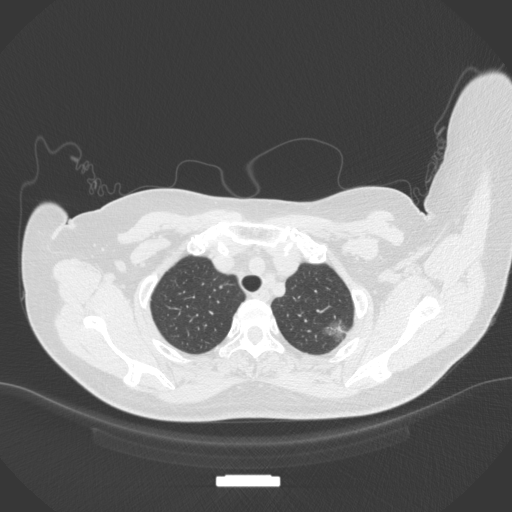
Chest CT, one axial slice; slice 315 of 386 in the series (ordered by position); 120 kVp; lung window (W 1500 / L -600 HU); 1 mm slice thickness; 512 × 512 image matrix, field of view 400 × 400 mm. Female patient, age 58 years. From the clinical record (not read from this slice): clinical TNM (as recorded): T1c N0 M0.
Annotated regions visible in this slice (rectangle marked by the reading radiologist):
- lung tumour (recorded histology: adenocarcinoma): bounding box [x1, y1, x2, y2] px = [322, 311, 355, 343]